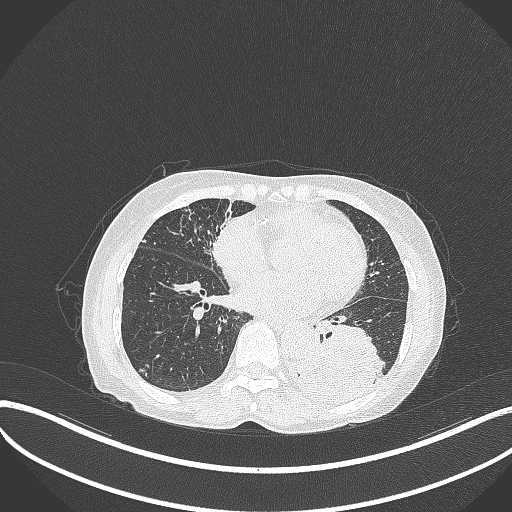
Chest CT, one axial slice; slice 120 of 370 in the series (ordered by position); reconstruction kernel B70f; 120 kVp; lung window (W 1500 / L -600 HU); 1 mm slice thickness; 512 × 512 image matrix, field of view 400 × 400 mm. Patient: female, 78 years. Case-level facts recorded for this patient, not image findings: clinical TNM (as recorded): T3 N0 M1.
Annotated regions visible in this slice (bounding box drawn by a radiologist):
- lung tumour (recorded histology: squamous cell carcinoma): bounding box (x1, y1, x2, y2) in pixels: (290, 317, 383, 393)